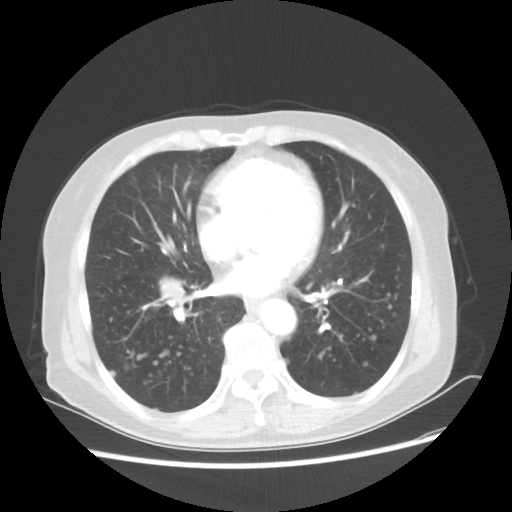
Chest CT, one axial slice. Position 23 of 56 along the scan axis. 80 kVp. Lung window (W 1500 / L -600 HU). 5 mm slice thickness. 512 × 512 image matrix, field of view 360 × 360 mm. Patient: female, 68 years. From the clinical record (not read from this slice): clinical TNM (as recorded): T1c N3 M0.
Annotated regions visible in this slice (rectangle marked by the reading radiologist):
- lung tumour (recorded histology: squamous cell carcinoma): box from (x=154, y=264) to (x=195, y=308) px